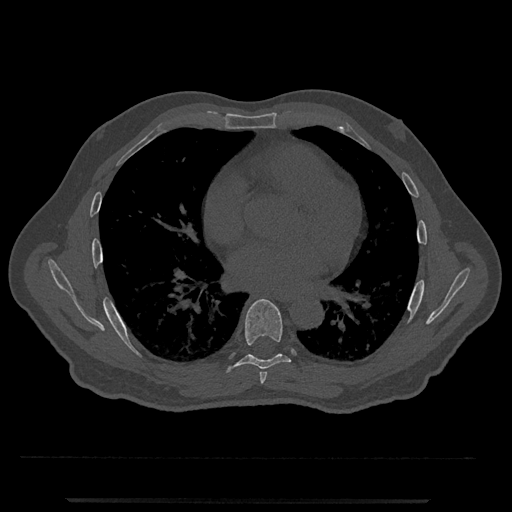
CT including the spine, one axial slice; position 683 of 797 along the scan axis; reconstruction kernel Br40s/3; 120 kVp; bone window (W 1800 / L 400 HU); 0.5 mm slice thickness; 512 × 512 image matrix. Male patient, age 63 years. From the clinical record (not read from this slice): primary cancer: prostate.
Outlined on this slice (semi-automatically segmented with operator editing):
- T6 vertebra: bounding box [x1, y1, x2, y2] px = [259, 372, 267, 384]
- T7 vertebra: [225, 299, 291, 373]